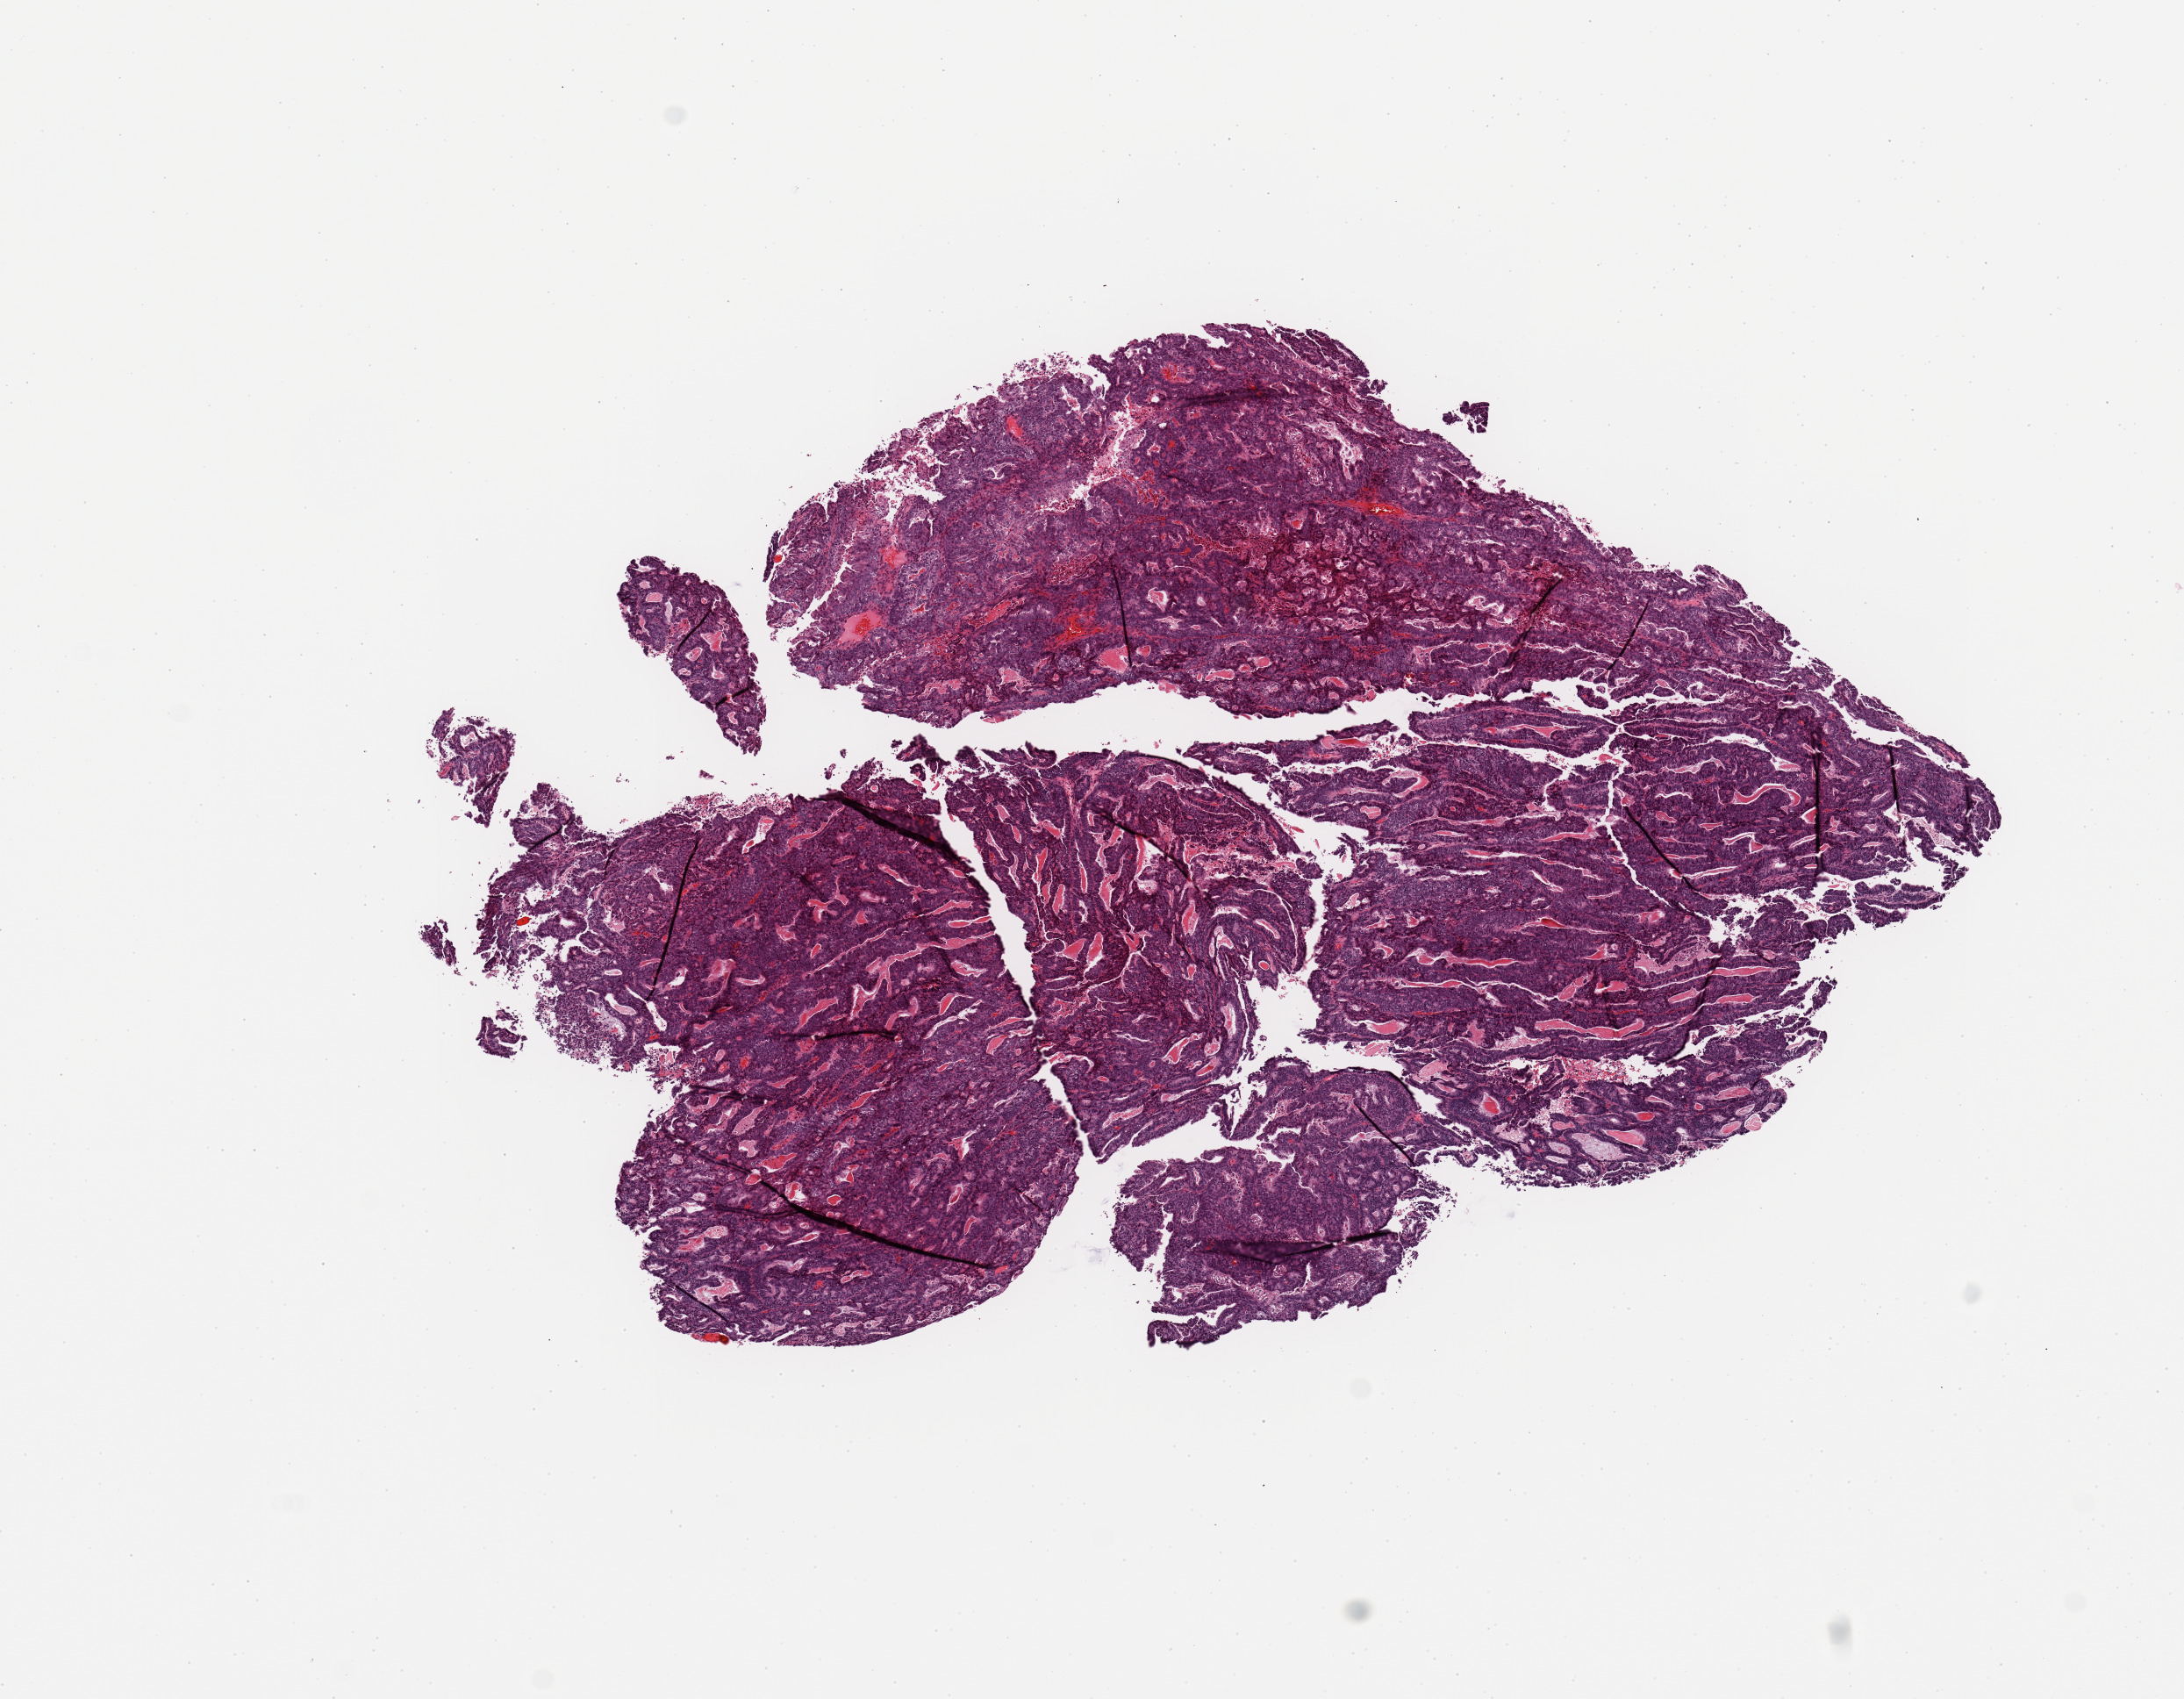
H&E whole-slide image — shown as a low-resolution overview of the whole scanned area (about 9.8 x 7.7 mm). Uterus, tumour tissue. 55-year-old female patient. Histologic grade: G1 (well differentiated).
* AJCC pathologic stage: III
* diagnosis: Endometrioid adenocarcinoma, NOS